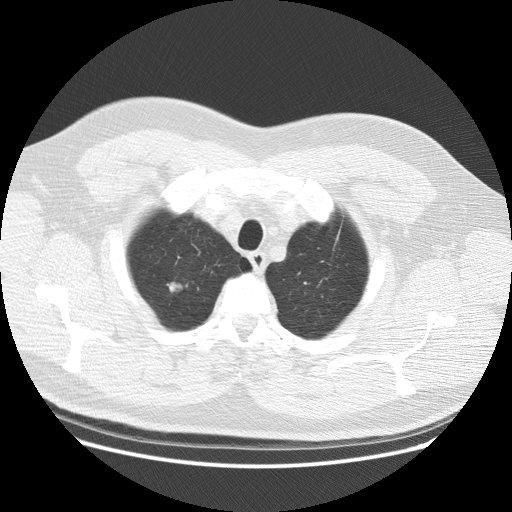
Low-dose screening chest CT, one axial slice. Position 97 of 111 along the scan axis. 120 kVp. Lung window (W 1500 / L -600 HU). 2.5 mm slice thickness. 512 × 512 image matrix, field of view 389 × 389 mm.
Structures marked on this image (outlined manually by an expert reader):
- lesion 1 (tumor, upper lobe of right lung): bounding box (x1, y1, x2, y2) in pixels: (168, 282, 187, 293)